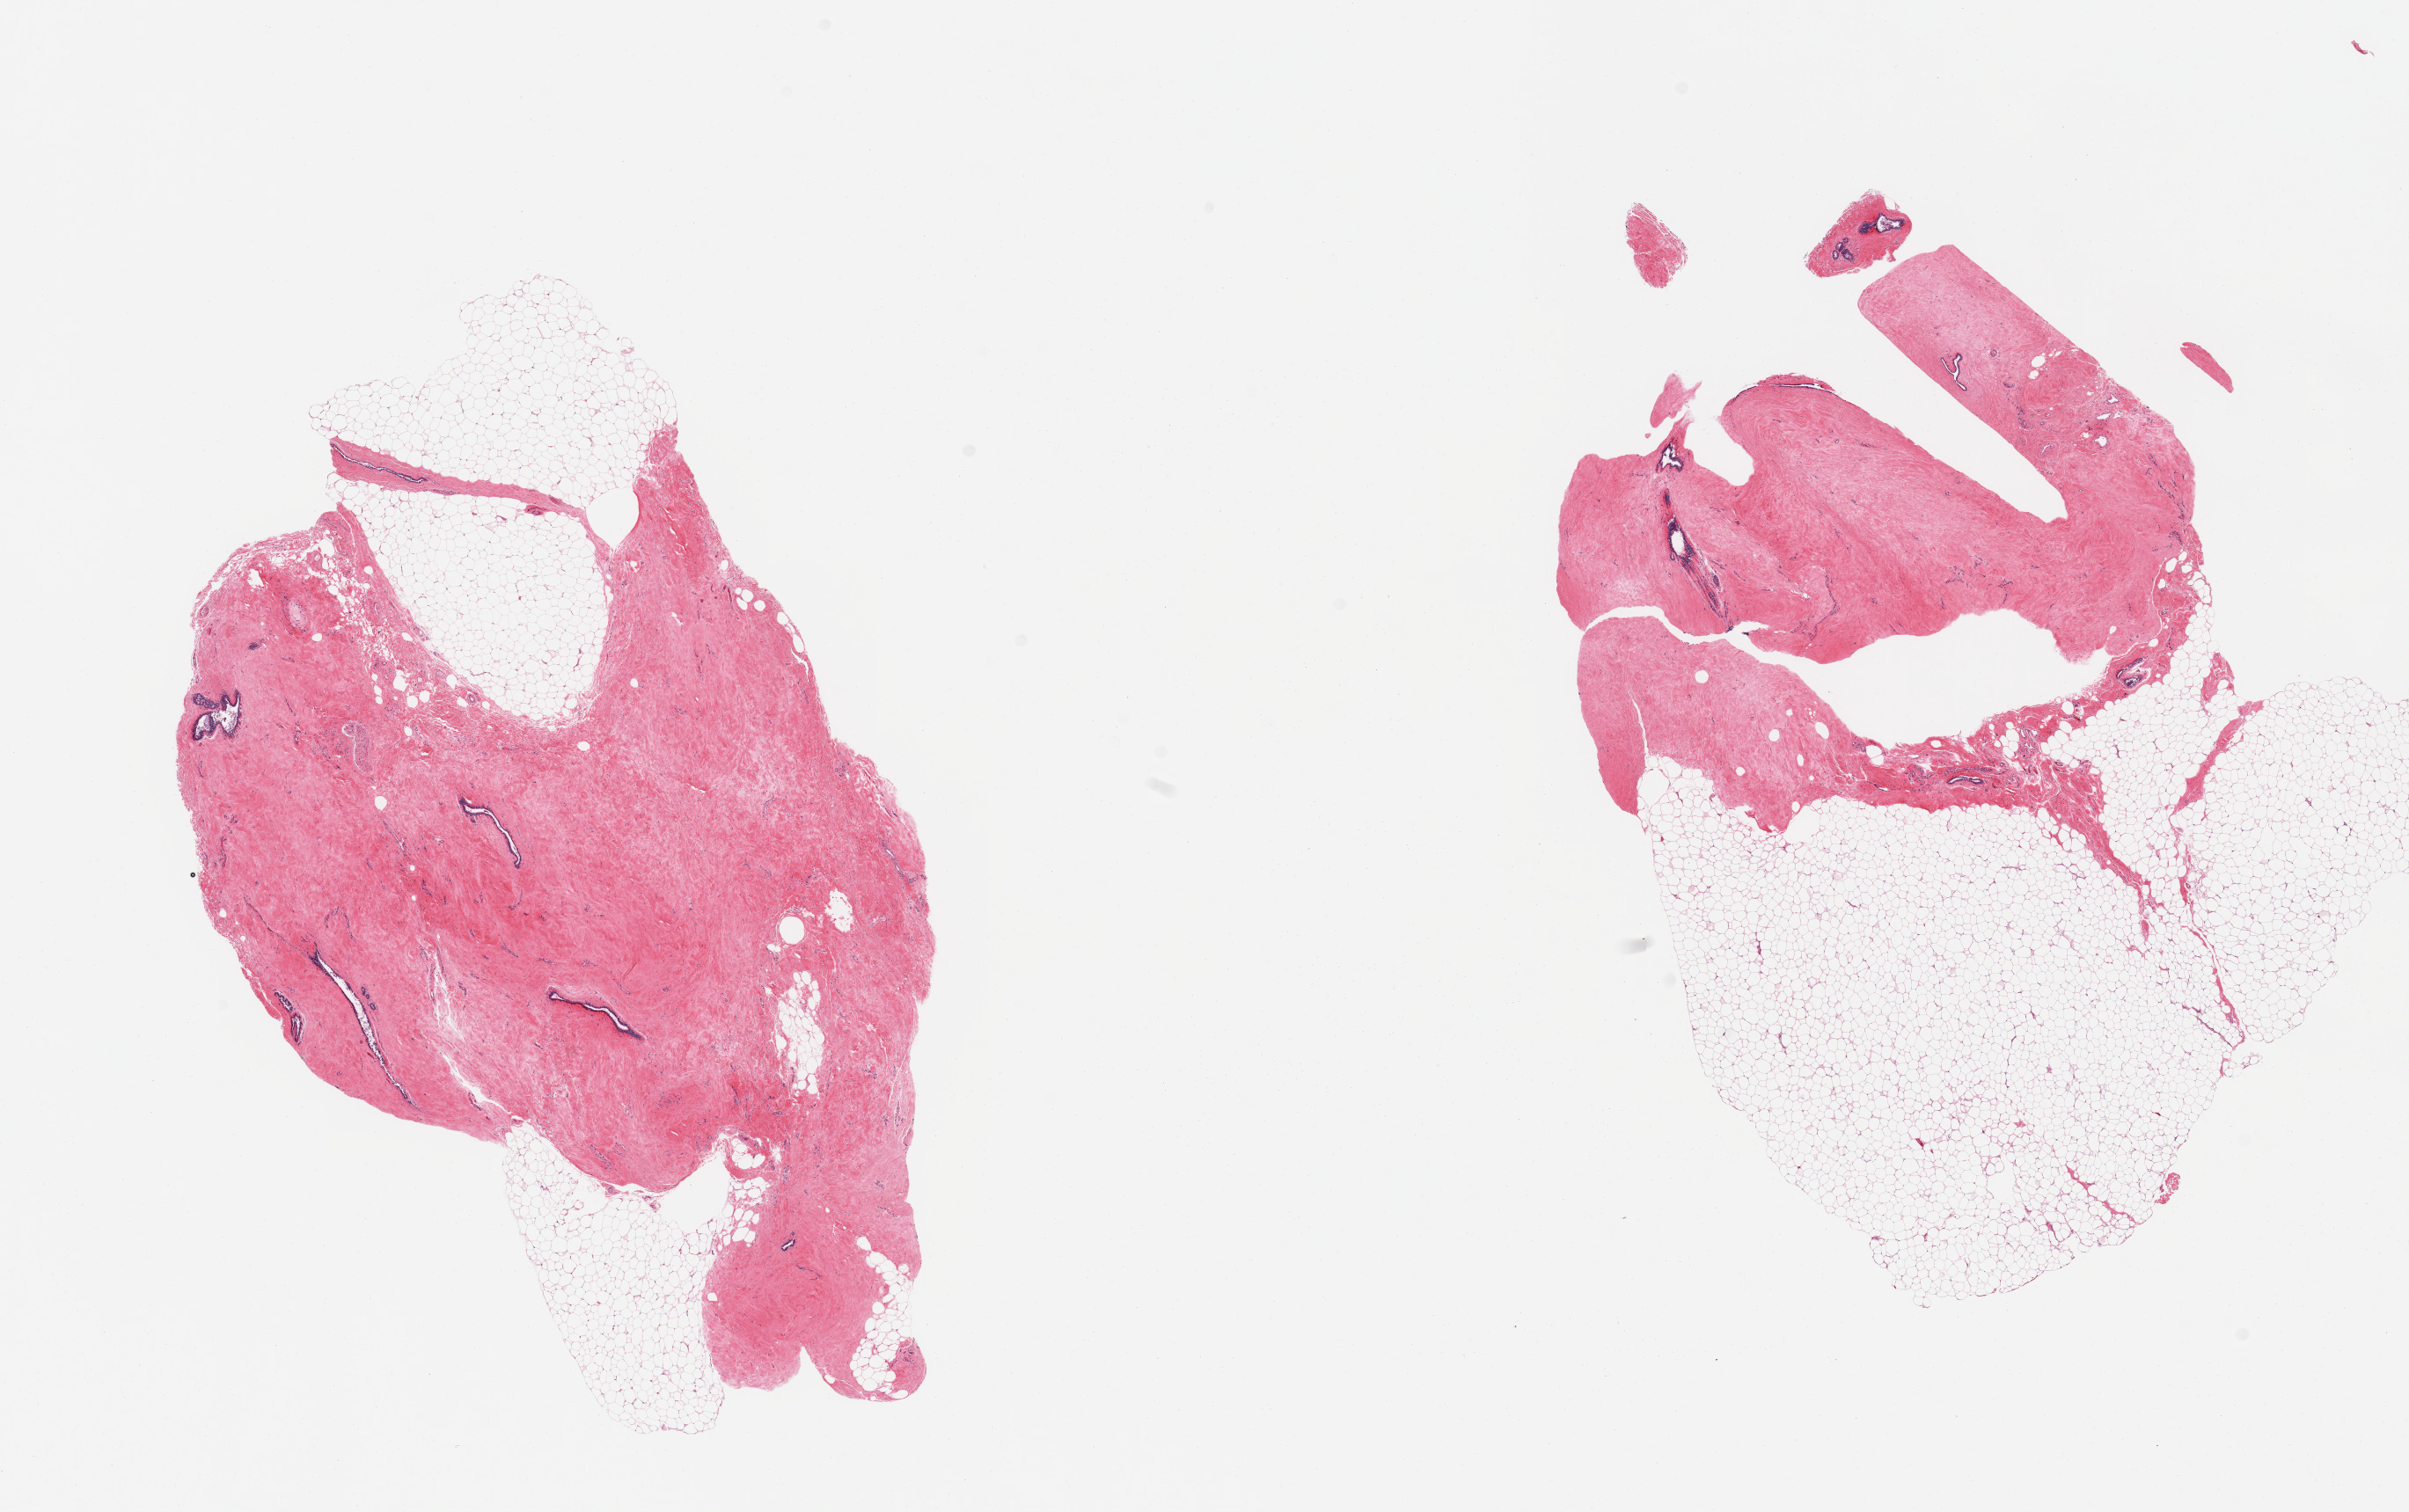
Whole-slide image, hematoxylin and eosin (H&E) stain, brightfield, shown as a low-resolution overview of the whole scanned area (about 21.7 x 13.6 mm, slide scanned at 20x). PAXgene-fixed, paraffin-embedded tissue. Section of breast (target tissue). Tissue donor sample. Donor: male.
Reviewer comment on this tissue sample: 2 pieces; dense fibrous connective tissue and scattered ductal structures with 30% and 50% attached fat.